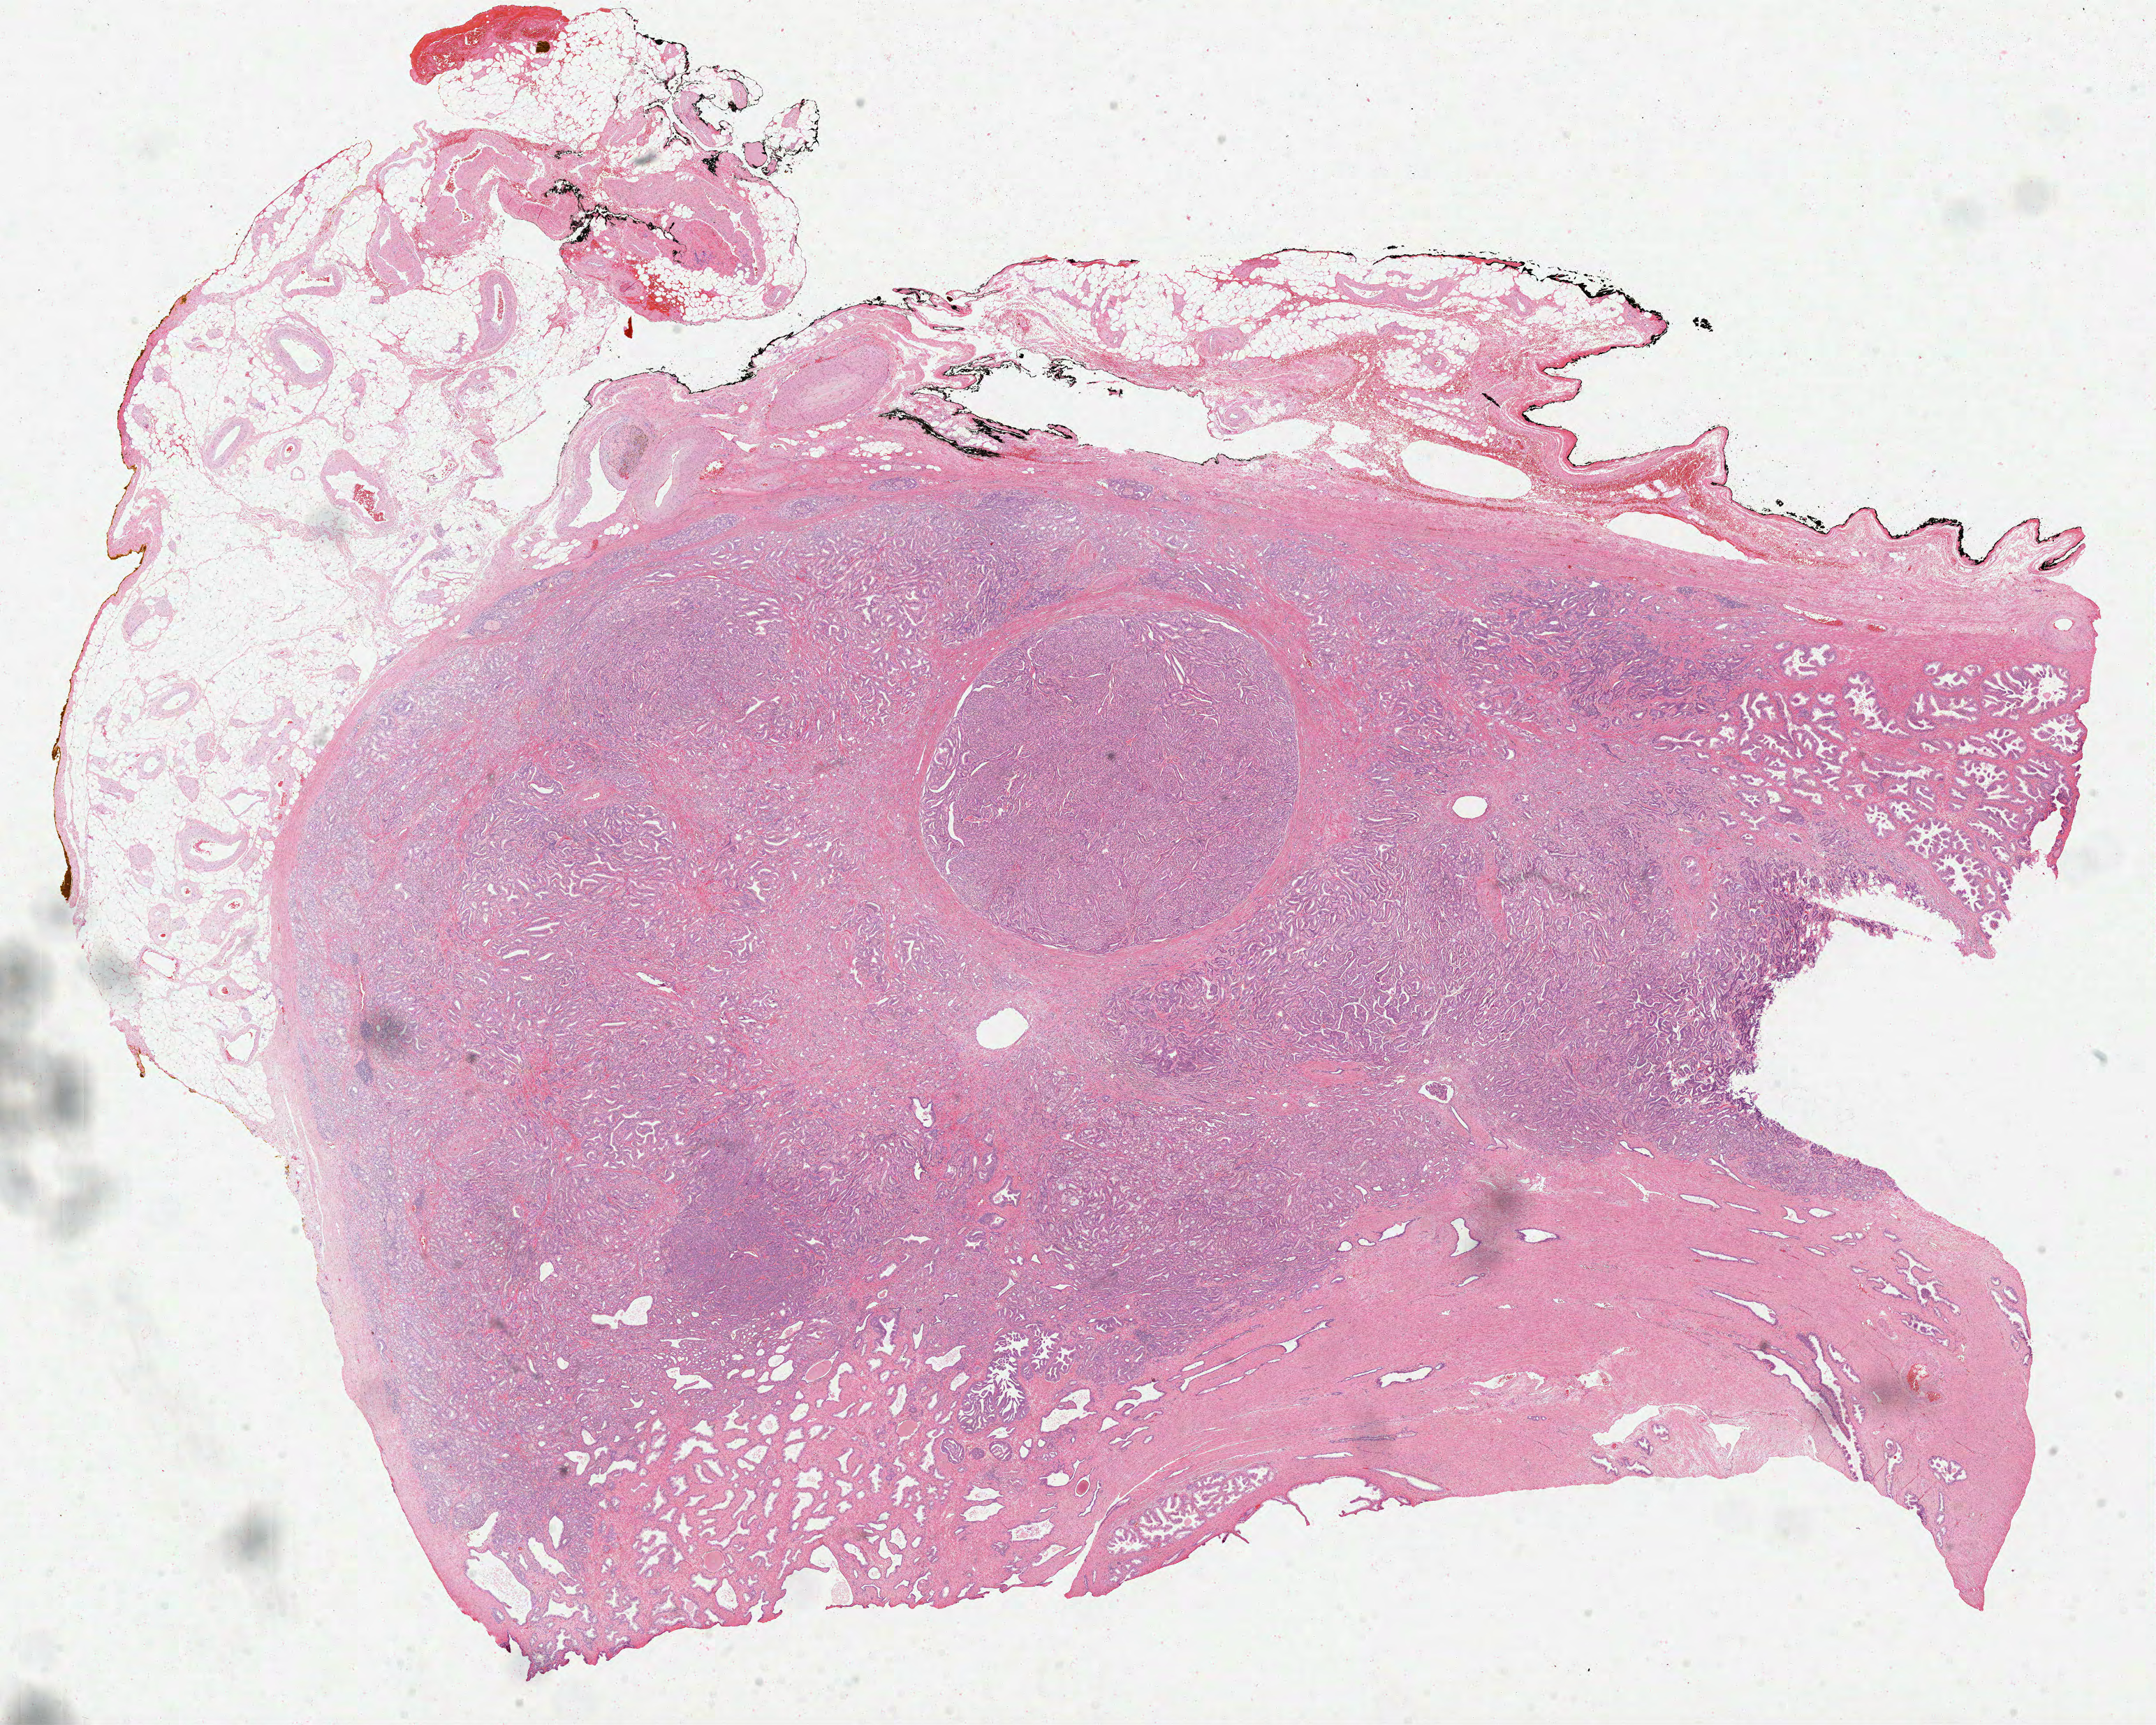
Hematoxylin and eosin (H&E) stained whole-slide image, a low-resolution overview of the entire scanned area, about 24.9 x 19.9 mm (acquisition: 40x scan). Formalin-fixed paraffin-embedded (FFPE) diagnostic section. Primary tumour sample from the prostate. Male patient; age at initial diagnosis 64 years. Gleason score: 7 (4+3).
* lymph nodes positive (case pathology): 0 of 6 examined
* pathologic diagnosis: Acinar cell carcinoma
* laterality: bilateral